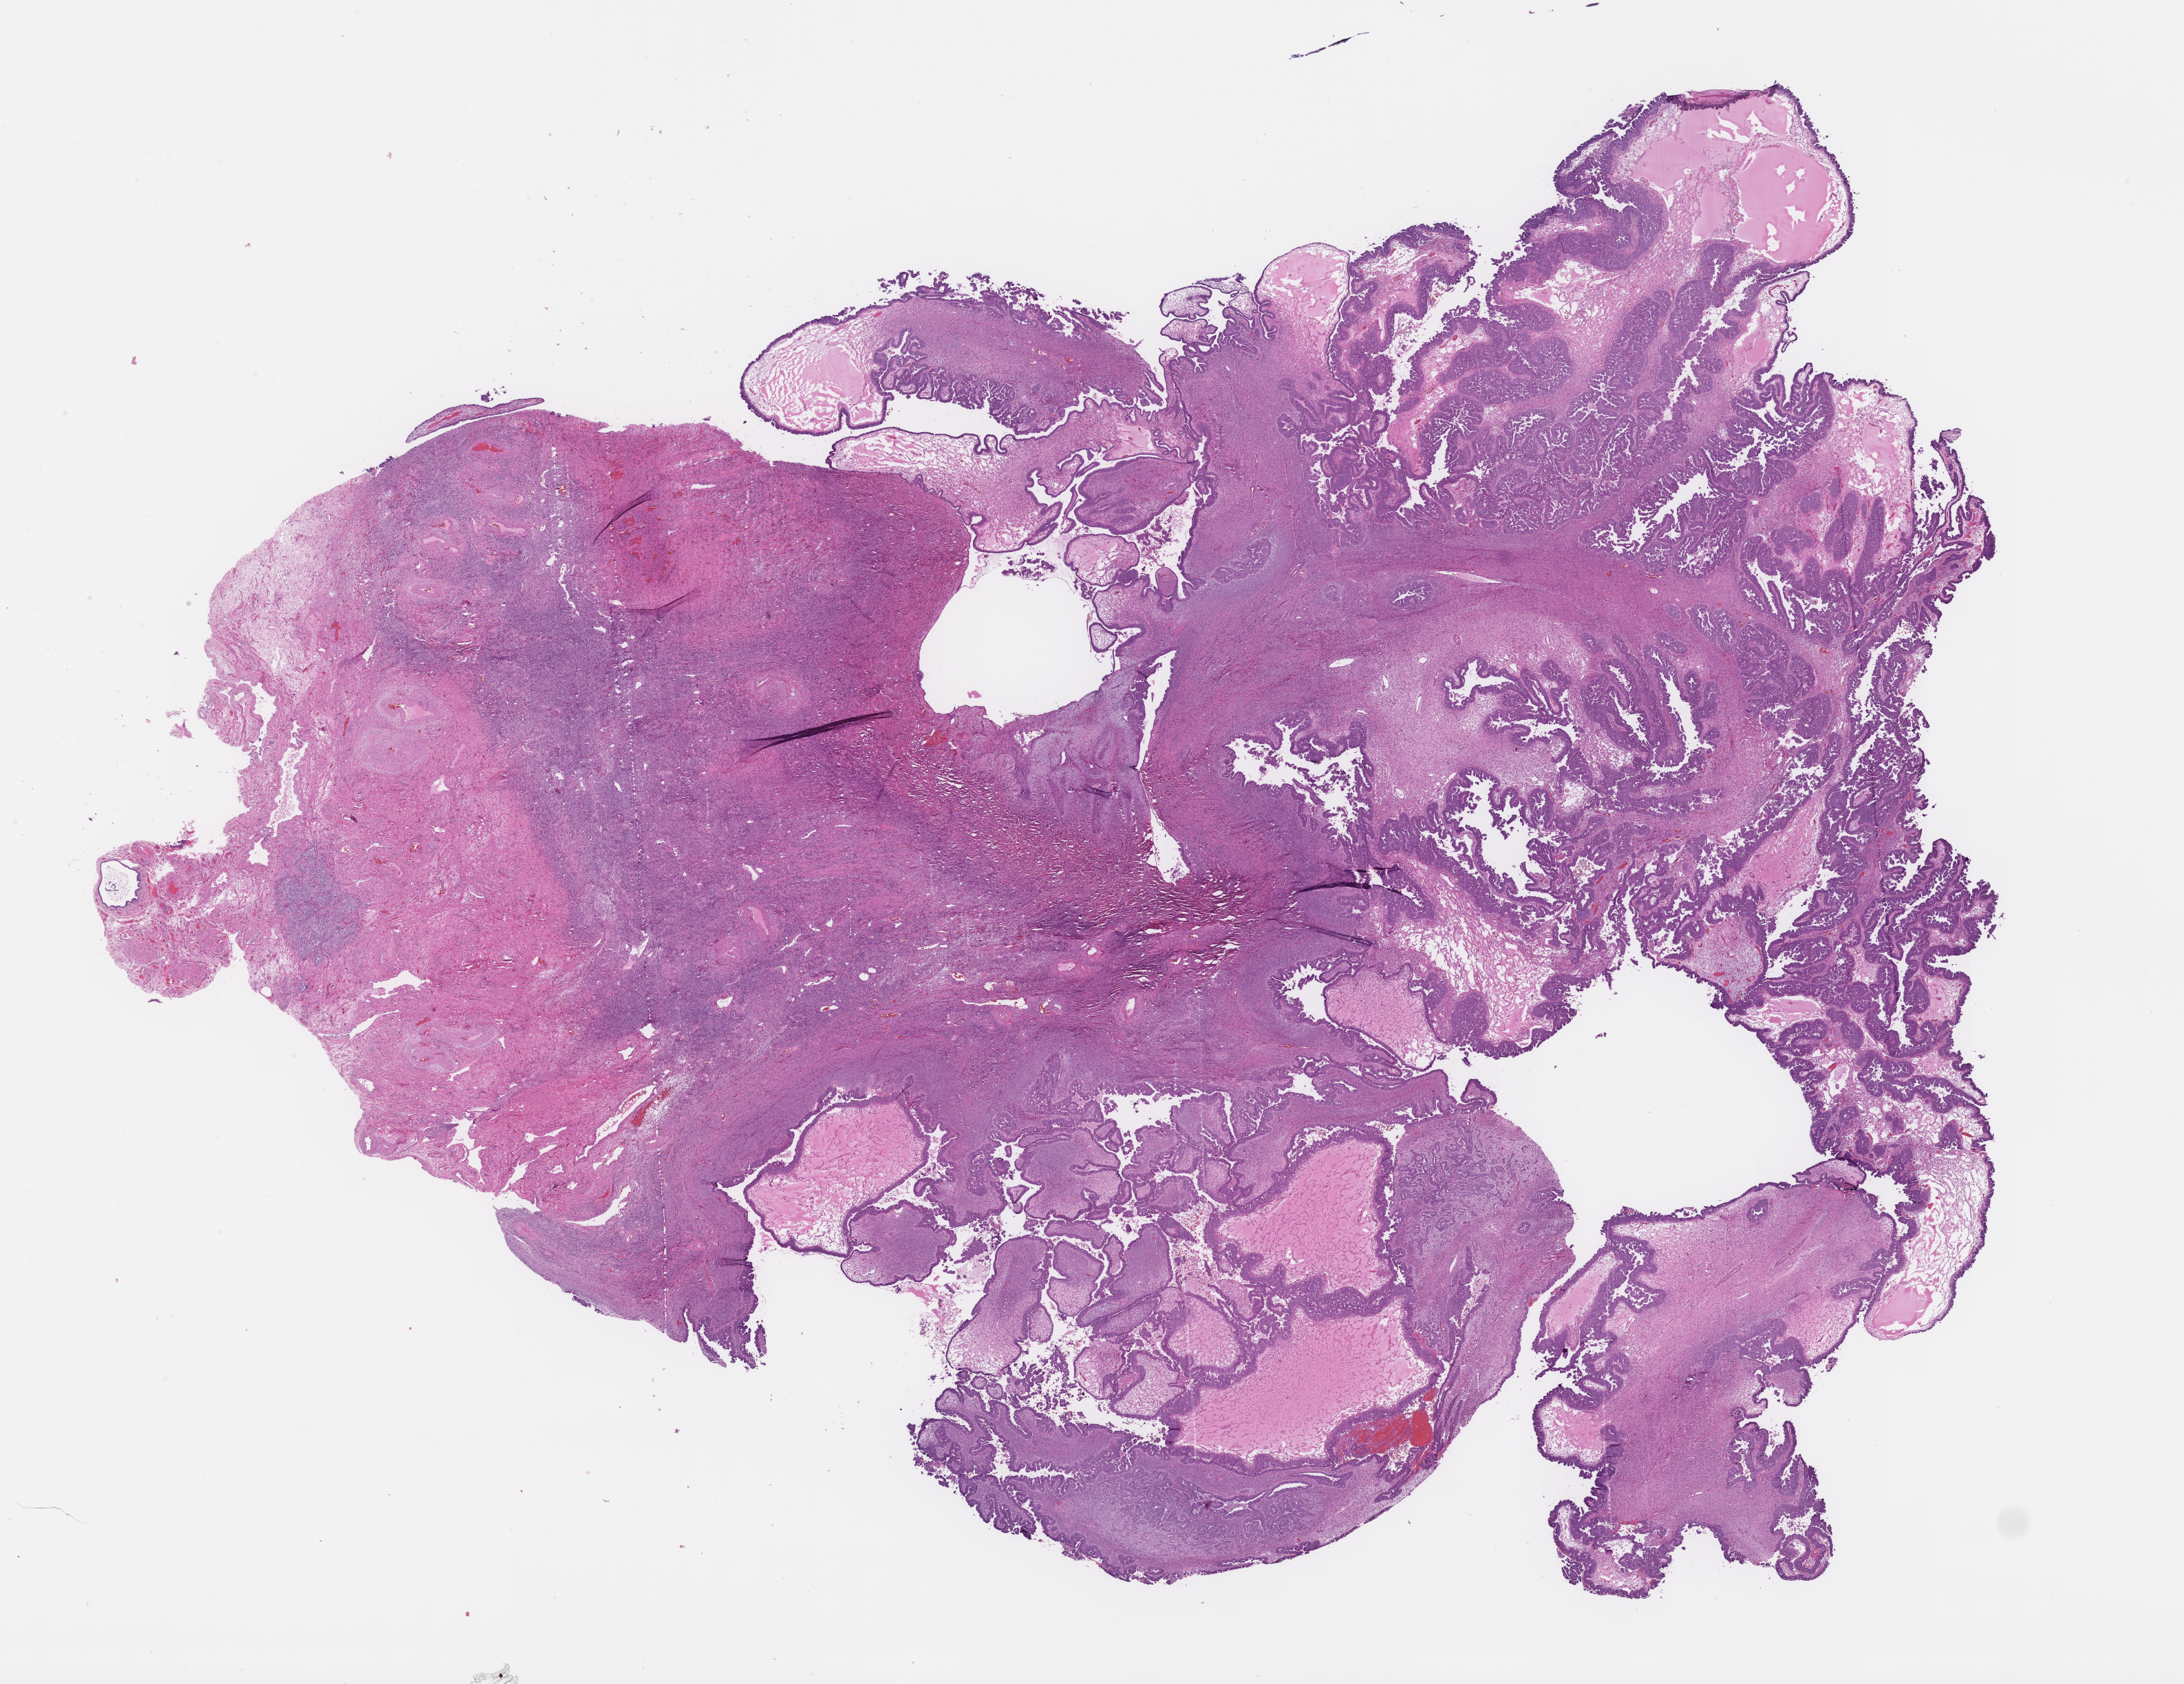
Digitized H&E-stained section — whole scanned area (about 25.6 x 19.8 mm) shown as a low-resolution overview, formalin-fixed paraffin-embedded section, site: fallopian tube. Female patient.
From a patient with: Ovarian Carcinoma.